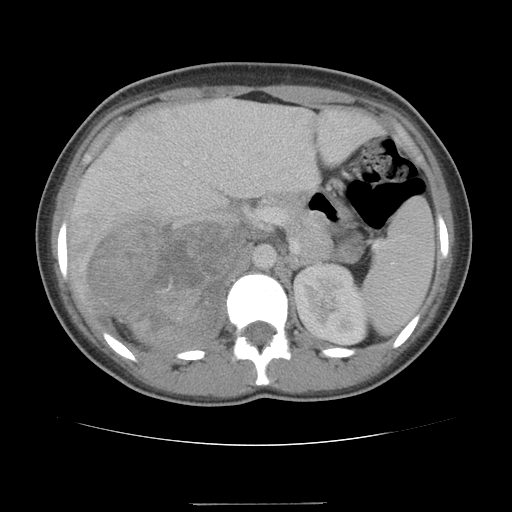
Contrast-enhanced abdominal CT, one axial slice; slice 71 of 100 in the series (ordered by position); reconstruction kernel STANDARD; 120 kVp; intravenous contrast given; soft-tissue window (W 400 / L 40 HU); 5 mm slice thickness; 512 × 512 image matrix, field of view 360 × 360 mm. Female patient, age 21 years. From the clinical record (not read from this slice): diagnosis: adrenocortical carcinoma; tumour side: right adrenal.
Annotated regions visible in this slice (semi-automatic segmentation, software-assisted and operator-edited):
- mass: bounding box (x1, y1, x2, y2) in pixels: (91, 222, 238, 348)